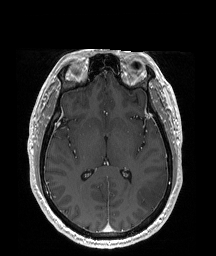
Brain MRI from a brain-tumour surgery series, one axial slice. Slice 99 of 192 in the series (ordered by position). T1-weighted post-contrast. 1 mm slice thickness. 216 × 256 image matrix, field of view 219 × 260 mm. From the clinical record (not read from this slice): histopathology: Glioblastoma; WHO grade: 4; IDH mutation: no.
Outlined on this slice (expert manual segmentation):
- tumour: bounding box [x1, y1, x2, y2] px = [139, 172, 168, 209]